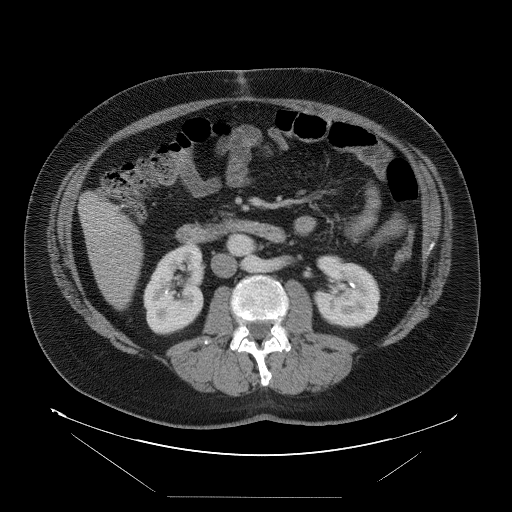
Contrast-enhanced abdominal CT, one axial slice. Slice 26 of 114 in the series (ordered by position). Soft-tissue window (W 400 / L 40 HU). 5 mm slice thickness. 512 × 512 image matrix. Male patient, age 61 years. From the clinical record (not read from this slice): diagnosis: colorectal cancer liver metastases, imaged before liver resection; multiple liver metastases: no; largest metastasis: 6.5 cm.
Annotated regions visible in this slice (manually delineated by an expert):
- liver: bounding box <81,193,143,309> (left, top, right, bottom; pixels)